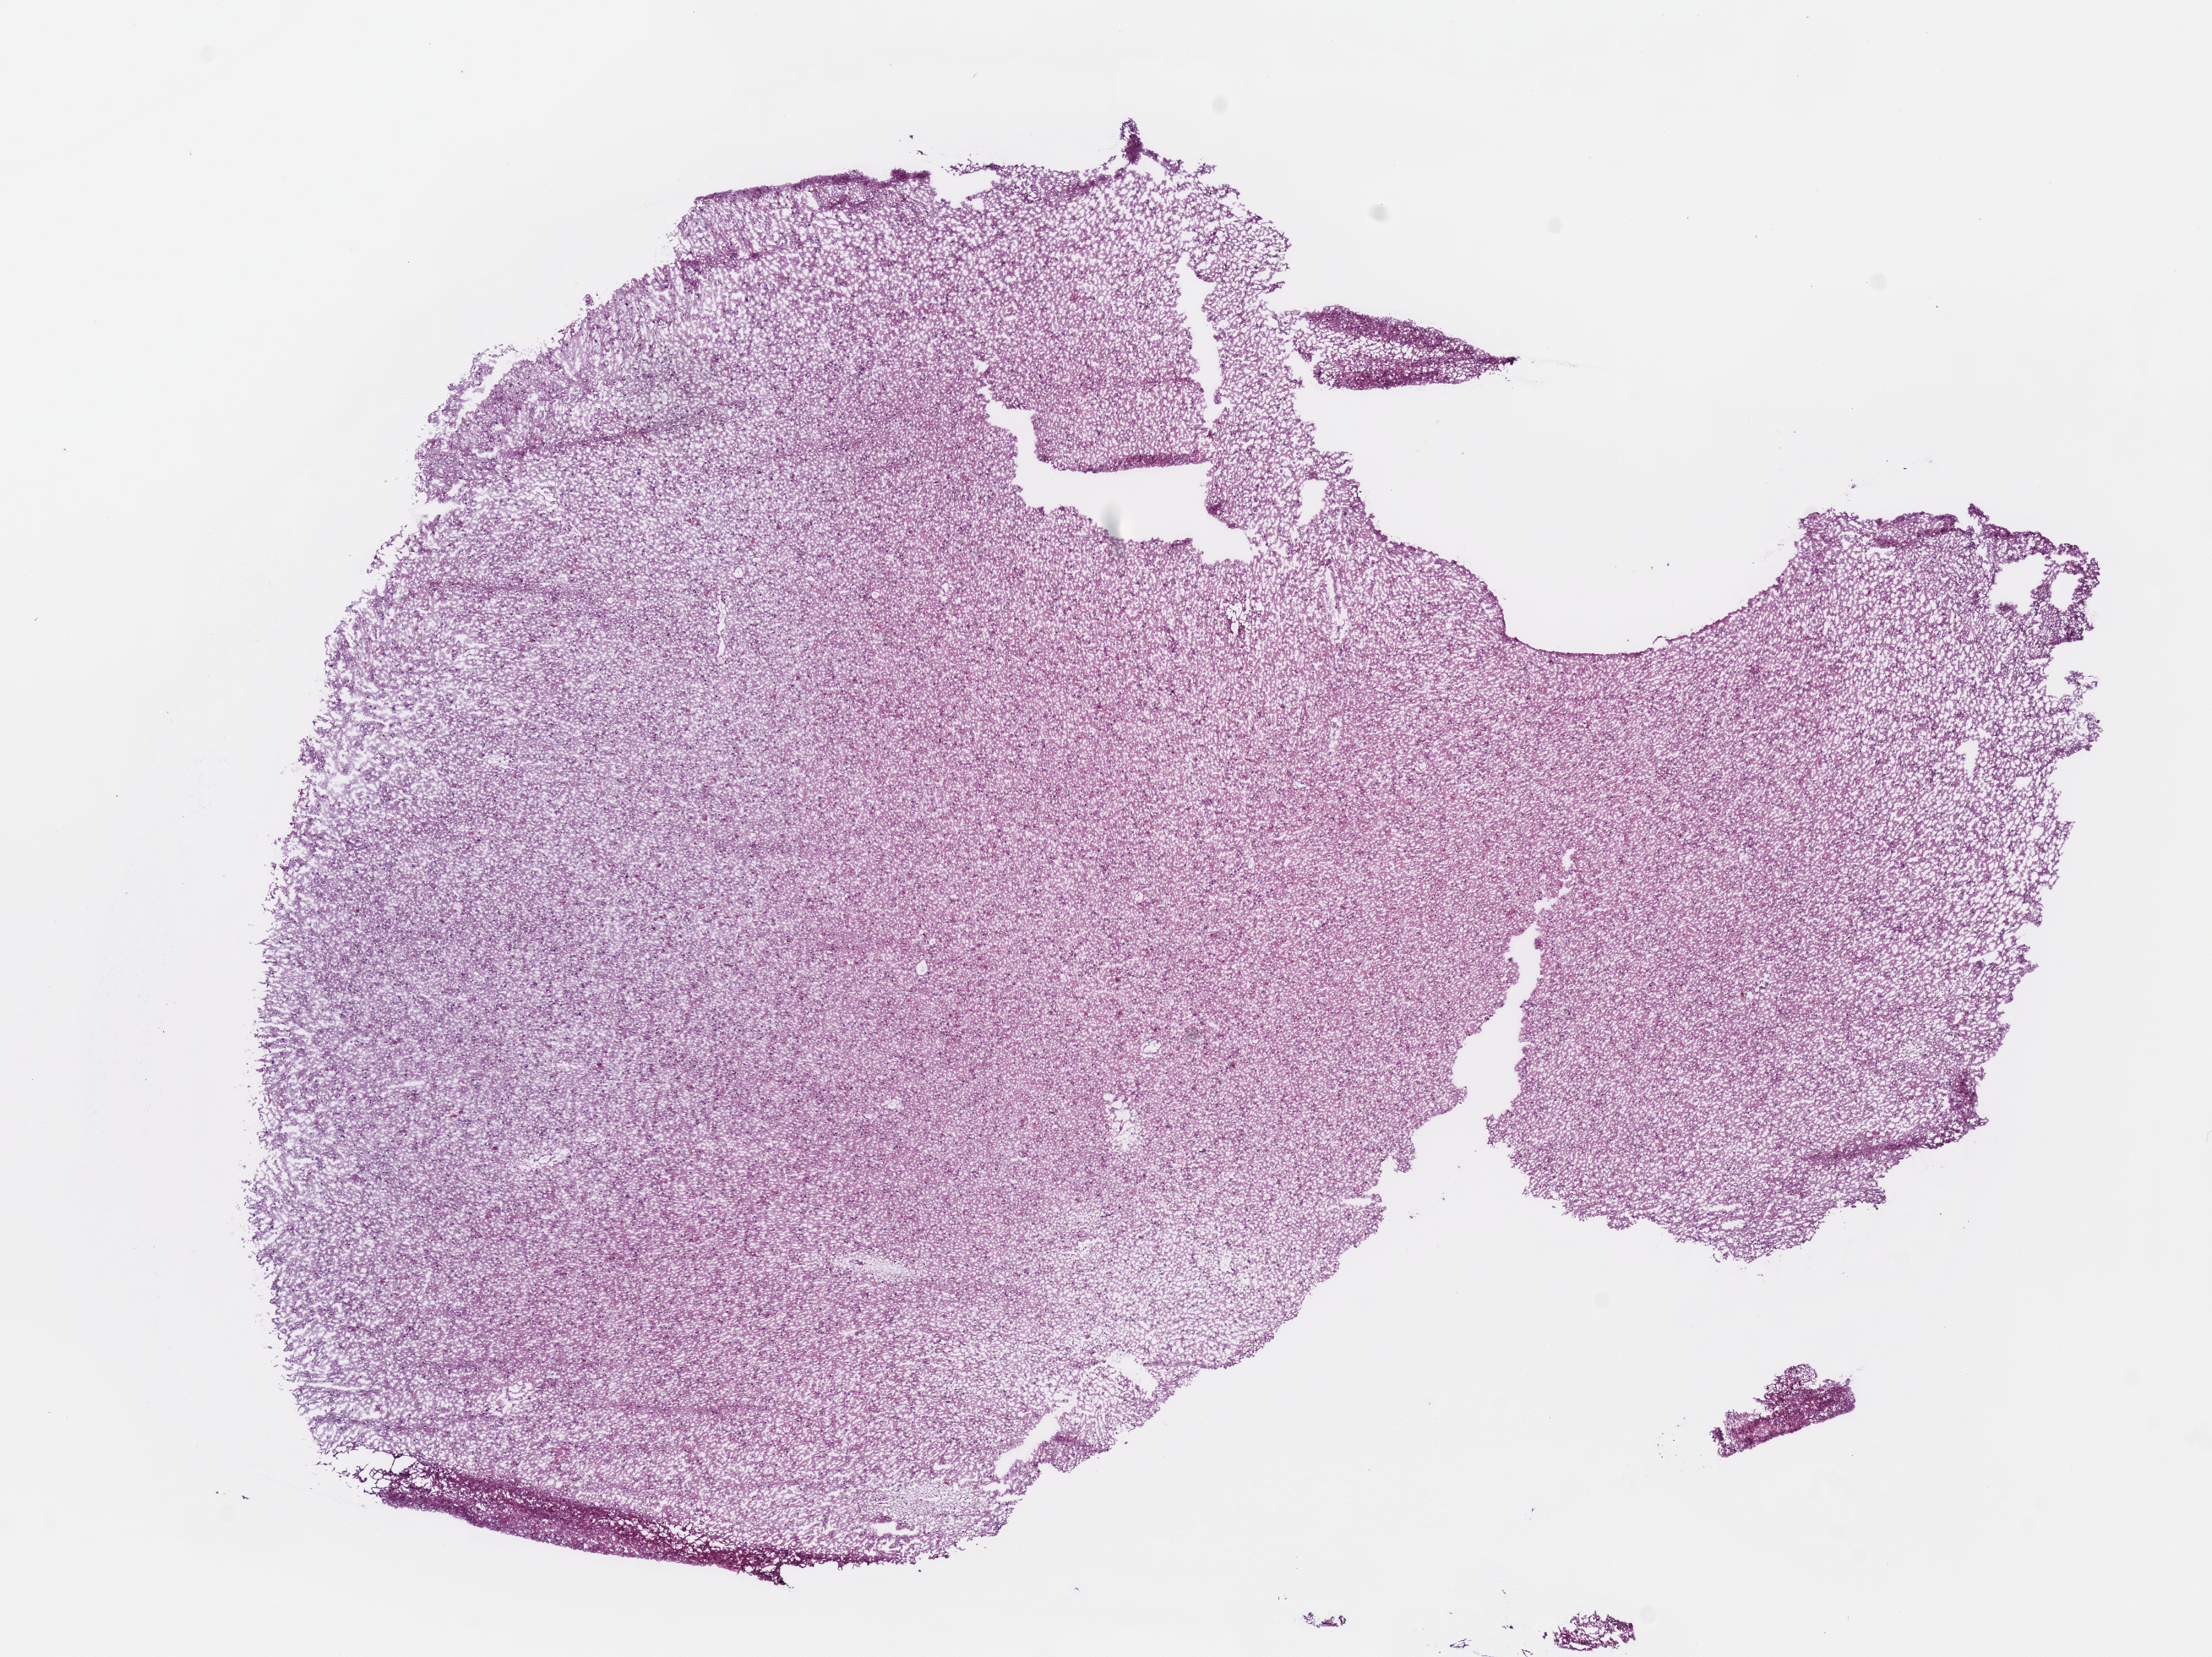
Digitized Hematoxylin and eosin (H&E) stained tissue section (whole slide), a low-resolution overview of the entire scanned area, about 10.3 x 7.7 mm; frozen section from the top of the tissue portion; sample: primary tumour, brain. Female patient; age at initial diagnosis 30 years. Histologic grade: G3 (poorly differentiated). Pathologist review of this section (percent, as recorded): tumour cells 100%, tumour nuclei 60%, normal cells 0%, stromal cells 0%, necrosis 0%.
Pathologic diagnosis: Astrocytoma, anaplastic.